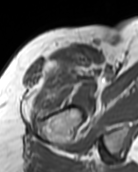
MRI of an extremity soft-tissue mass, one axial slice; slice 83 of 99 in the series (ordered by position); MR volume resampled by the dataset authors to the PET/CT grid (not the native acquisition matrix); 3.27 mm slice thickness; 138 × 172 image matrix. Female patient. Case-level facts recorded for this patient, not image findings: histological type: pleiomorphic undifferentiated sarcoma; grade: high; site of the primary tumour: right quadricep.
Outlined on this slice (expert contour drawn on MRI and transferred to this co-registered scan by the dataset authors):
- gross tumour volume including surrounding oedema: box from (x=28, y=61) to (x=86, y=119) px